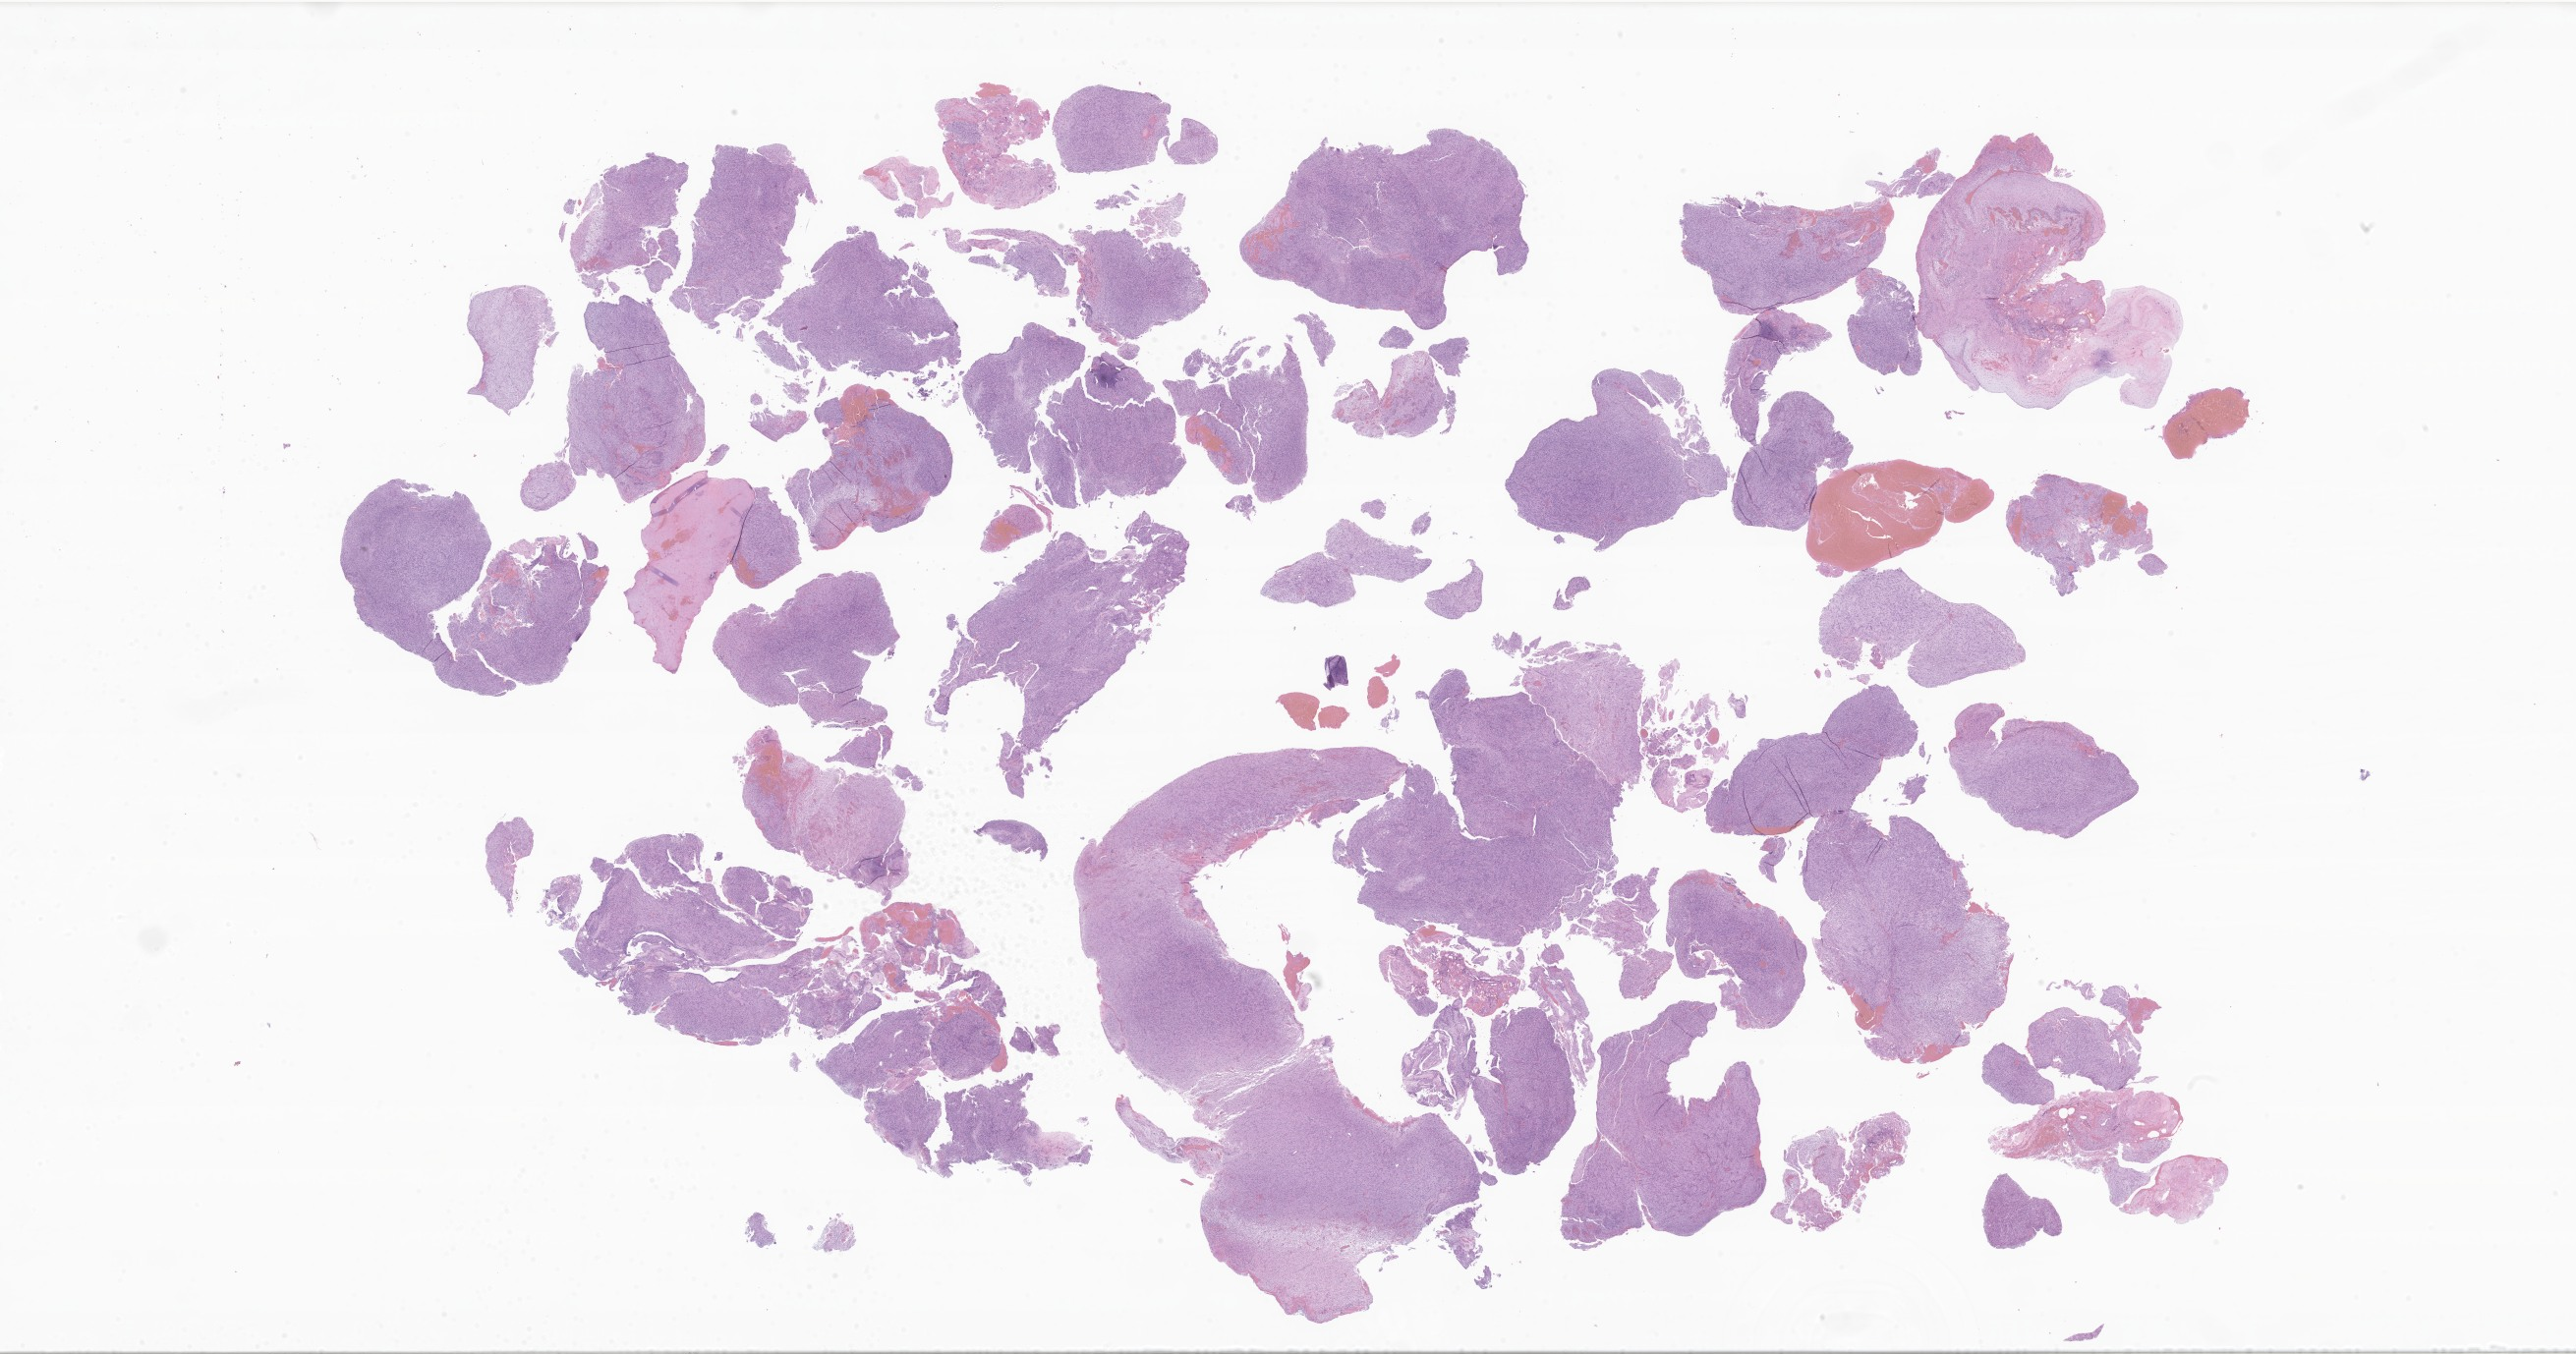
Digitized hematoxylin and eosin (H&E)-stained section of tumor tissue from the brain — whole scanned area (about 44.2 x 23.2 mm) shown as a low-resolution overview, formalin-fixed paraffin-embedded section. Female patient, age 123 months (10 years 3 months).
Diagnosis (ICD-O-3 morphology term): Schwannoma, NOS.